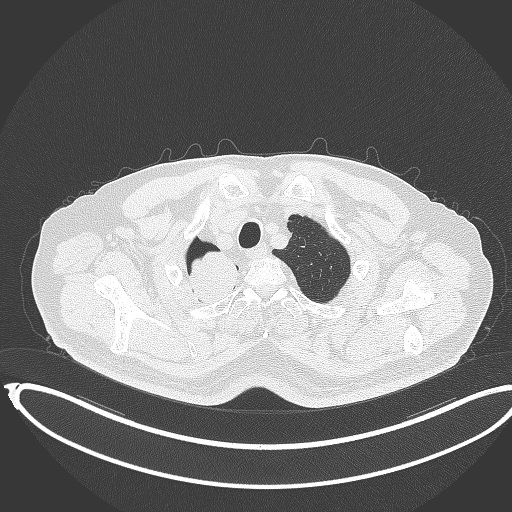
Chest CT, one axial slice; slice 333 of 403 in the series (ordered by position); 120 kVp; lung window (W 1500 / L -600 HU); 512 × 512 image matrix, field of view 436 × 436 mm. Patient: male, 68 years. From the clinical record (not read from this slice): clinical TNM (as recorded): T2a N0 M0.
Structures marked on this image (bounding box drawn by a radiologist):
- lung tumour (recorded histology: adenocarcinoma): bounding box <182,245,246,312> (left, top, right, bottom; pixels)